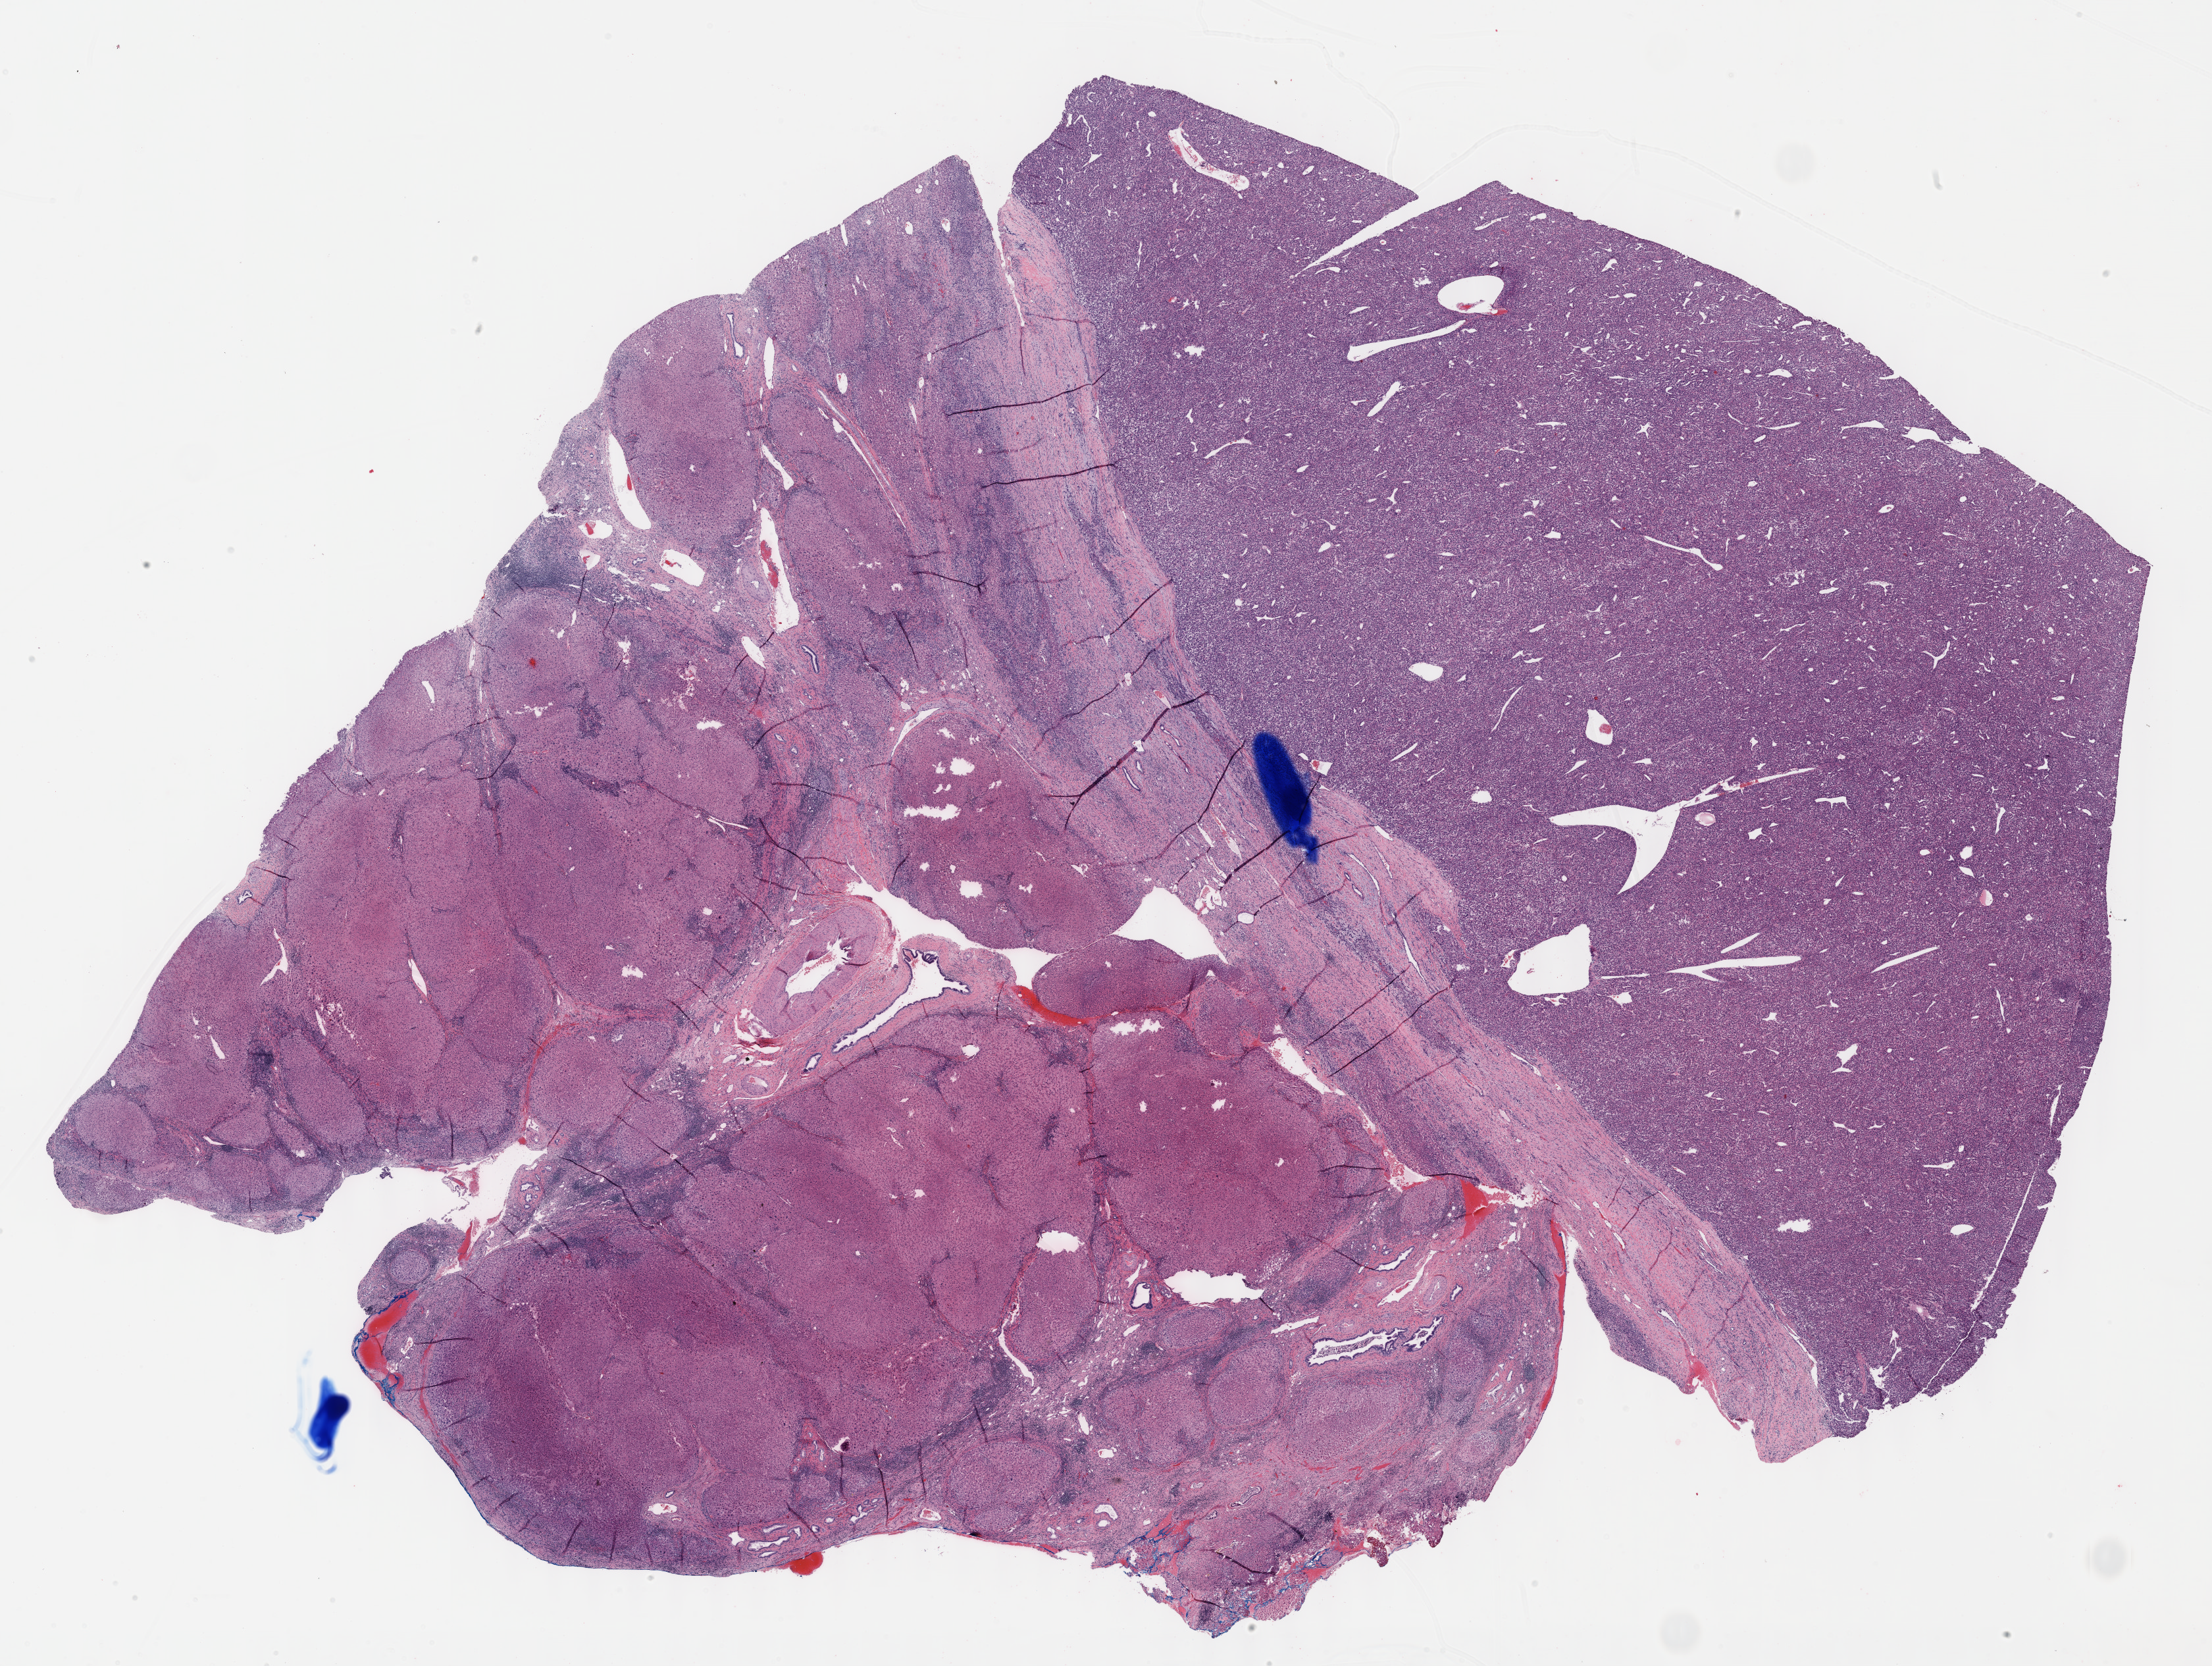
H&E-stained whole-slide image — shown as a low-resolution overview of the whole scanned area (about 27.2 x 20.5 mm). Formalin-fixed paraffin-embedded (FFPE) diagnostic section. Liver, primary tumour sample. Patient: female, age at initial diagnosis 79 years.
Histologic diagnosis: Hepatocellular carcinoma, NOS.